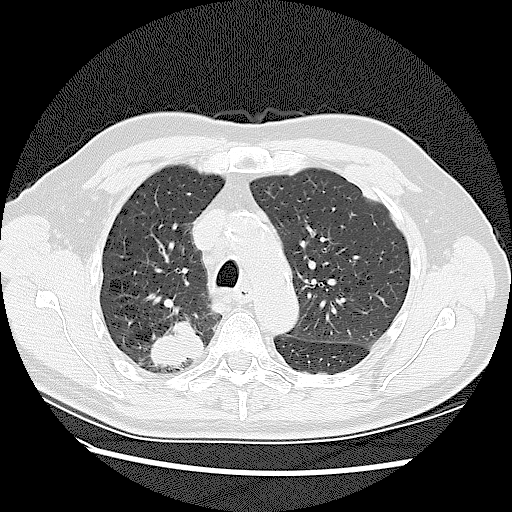
Chest CT (low-dose screening protocol), one axial image; baseline annual screen; lung window (W 1500 / L -600 HU); 2.5 mm slice thickness; lung (sharp) reconstruction kernel (LUNG); 120 kVp; 512 × 512 image matrix, field of view 360 × 360 mm. Male, age 72 years at enrolment.
• Expert reader's lesion annotation, bounding box (x1, y1, x2, y2) in pixels: (140, 312, 213, 377).
• The screening reader recorded 2 non-calcified nodules or masses ≥4 mm on this exam (right upper lobe, right upper lobe); which of them this box marks is not recorded.
• Official screen result: positive, change unspecified: nodule(s) >= 4 mm or enlarging nodule(s), mass(es), or other non-specific abnormalities suspicious for lung cancer.
• Later outcome: lung cancer diagnosed 42 days after this screen — adenocarcinoma, NOS, right upper lobe, stage IV (AJCC 6th edition), 45 mm at pathology.